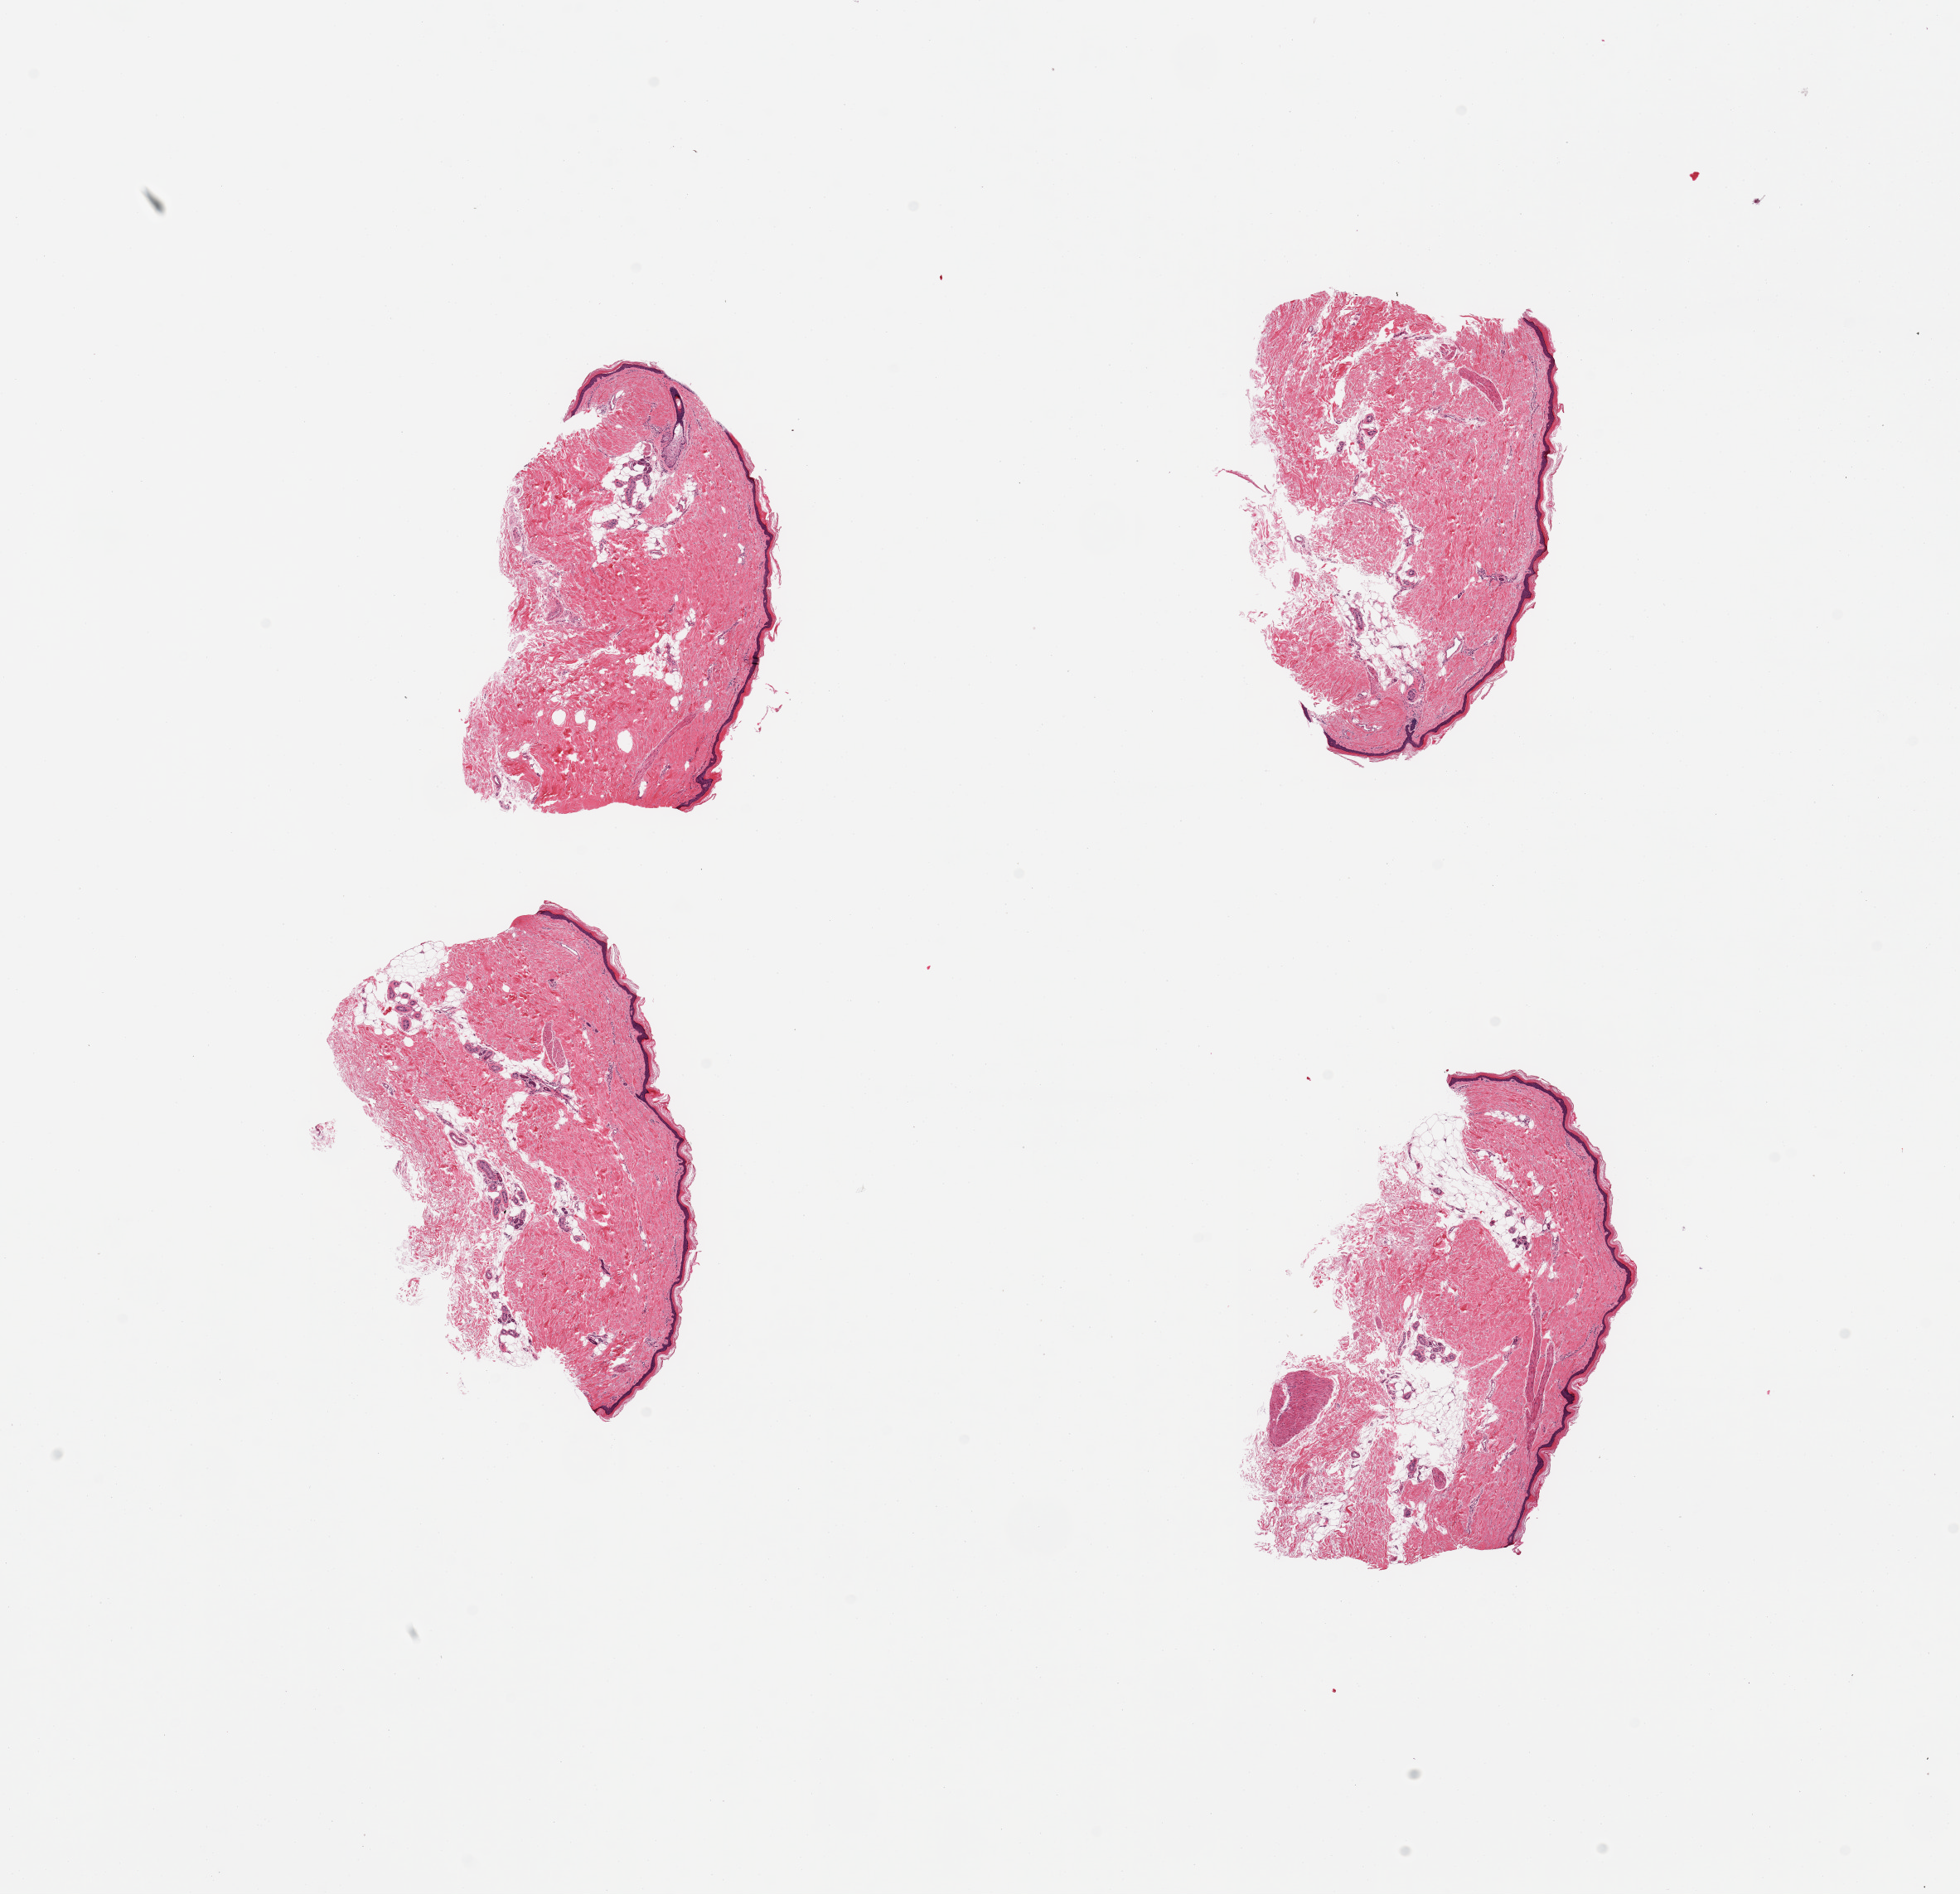
Digitized H&E-stained section, a low-resolution overview of the entire scanned area, about 18.7 x 18.1 mm, PAXgene-fixed paraffin-embedded (PFPE) section, sampled site (target tissue): skin of lower leg, donor tissue sample. Donor: male.
Review note (as recorded): 4 pieces, no dermal fat, squamous epithelium is ~30-35 microns.